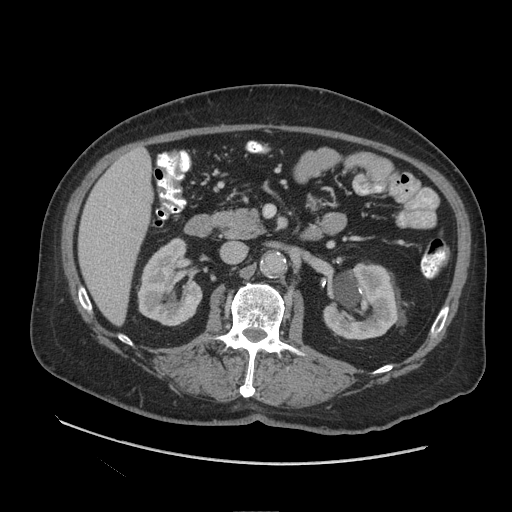
Contrast-enhanced abdominal CT (liver protocol), one axial slice; position 38 of 109 along the scan axis; reconstruction kernel STANDARD; 140 kVp; soft-tissue window (W 400 / L 40 HU); 512 × 512 image matrix, field of view 420 × 420 mm. From the clinical record (not read from this slice): diagnosis: hepatocellular carcinoma (patient treated with transarterial chemoembolisation; whether this scan precedes or follows treatment is not stated here); TNM stage (as recorded): Stage-I; Child-Pugh class: A.
Structures marked on this image (semi-automatically segmented with operator editing):
- liver parenchyma outside the tumour (the mass and vessels are separate outlines, so this box may not span the whole liver): box from (x=78, y=148) to (x=152, y=324) px